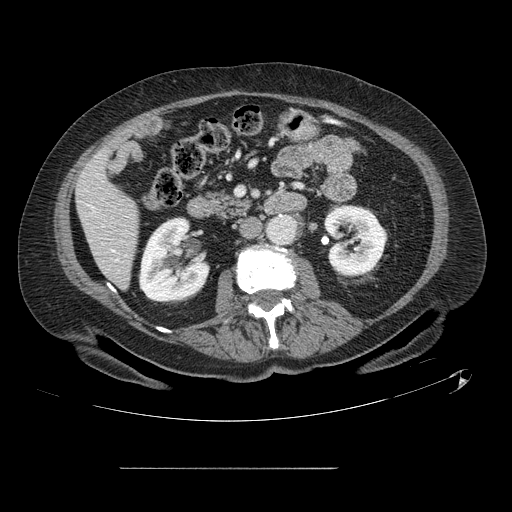
Contrast-enhanced abdominal CT, one axial slice. Position 36 of 148 along the scan axis. 120 kVp. Intravenous contrast given. Soft-tissue window (W 400 / L 40 HU). 512 × 512 image matrix. Female patient, age 75 years. Case-level facts recorded for this patient, not image findings: diagnosis: colorectal cancer liver metastases, imaged before liver resection; multiple liver metastases: no; largest metastasis: 2.4 cm.
Annotated regions visible in this slice (manually delineated by an expert):
- liver: bounding box [x1, y1, x2, y2] px = [77, 152, 138, 287]
- planned liver remnant (the part of the liver to remain after resection): [77, 152, 138, 287]